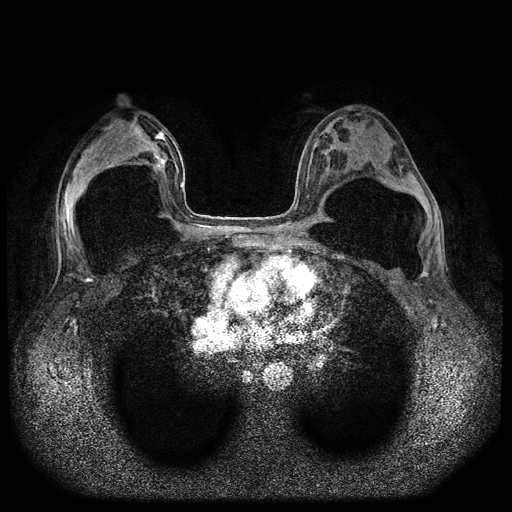
Breast MRI (dynamic contrast-enhanced, multi-phase), one axial slice. Position 51 of 116 along the scan axis. Dynamic contrast-enhanced series, time point 2 of 5 at this slice position (early post-contrast). 1.5 T. TE 2.6 ms, TR 5.4 ms. 2 mm slice thickness. 512 × 512 image matrix, field of view 340 × 340 mm. Female patient, age 42 years.
Annotated regions visible in this slice (semi-automatic segmentation, software-assisted and operator-edited):
- breast lesion (labelled 'tumour' in the annotation; benign lesions carry a separate 'benign' label): bounding box <155,131,167,165> (left, top, right, bottom; pixels)